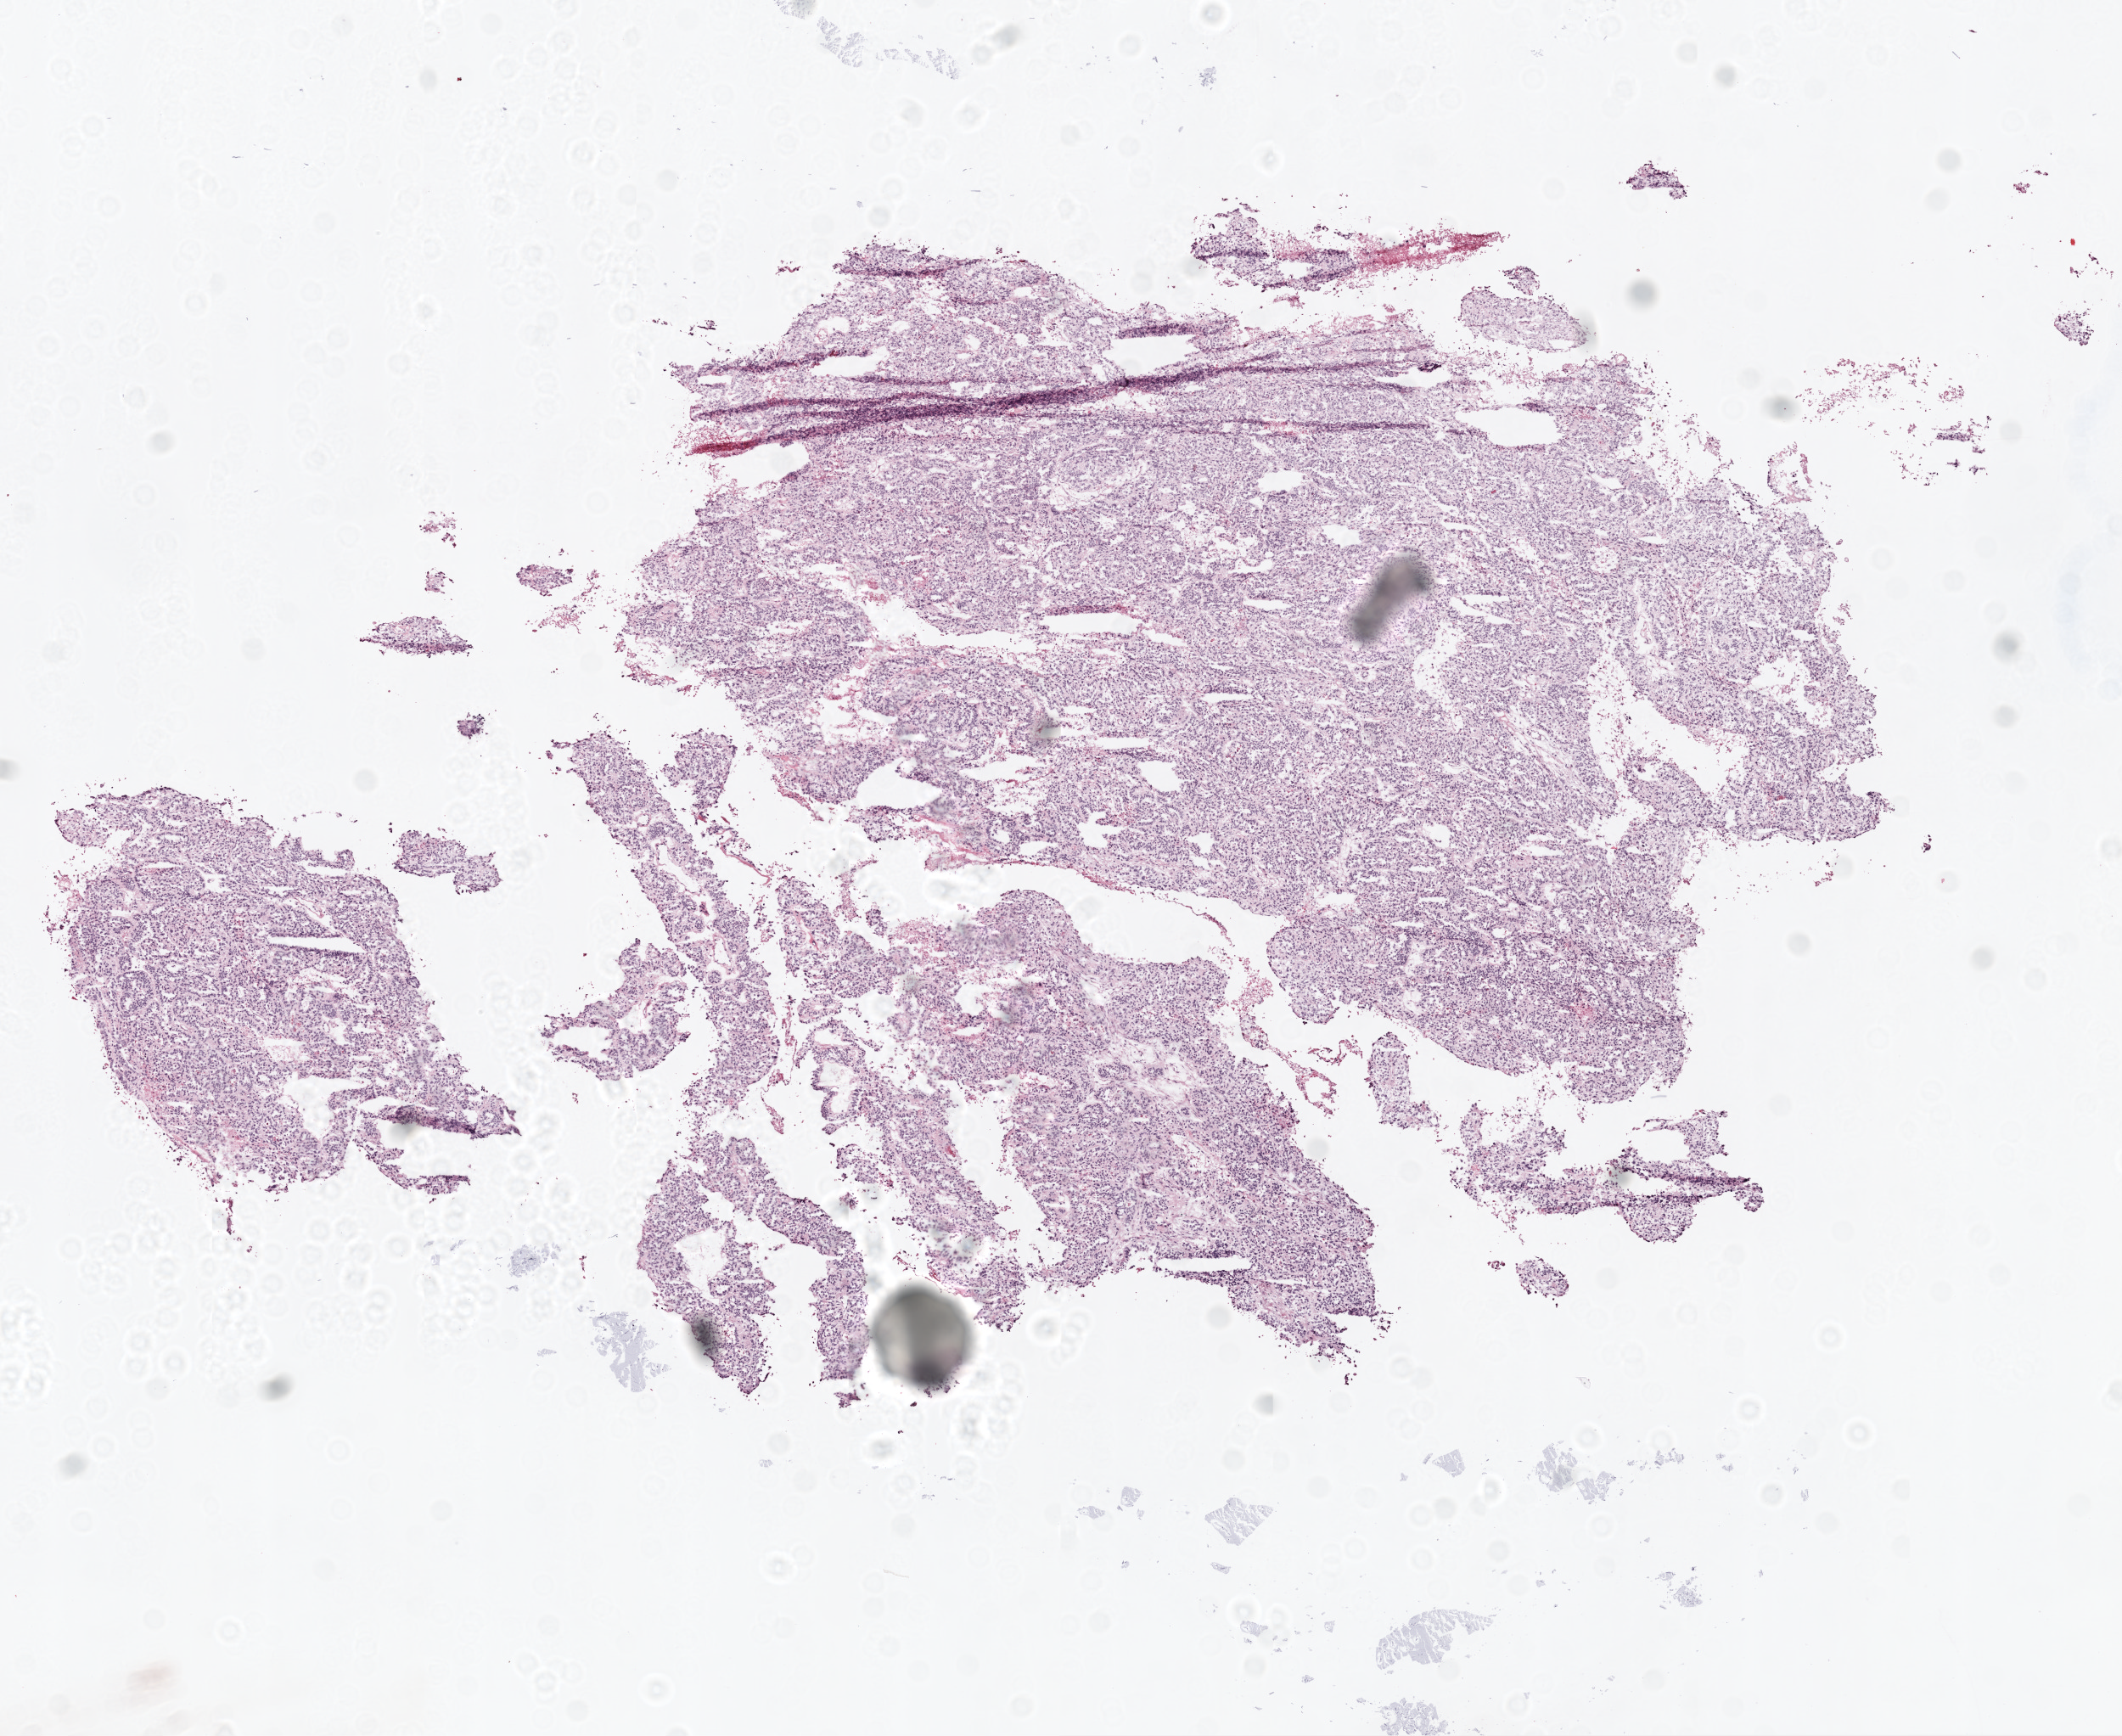
H&E whole-slide image — a low-resolution overview of the entire scanned area, about 10.0 x 8.2 mm; frozen section from the top of the tissue portion; primary tumour sample from the ovary. Patient: female, age at initial diagnosis 52 years.
Diagnosis: Serous cystadenocarcinoma, NOS.